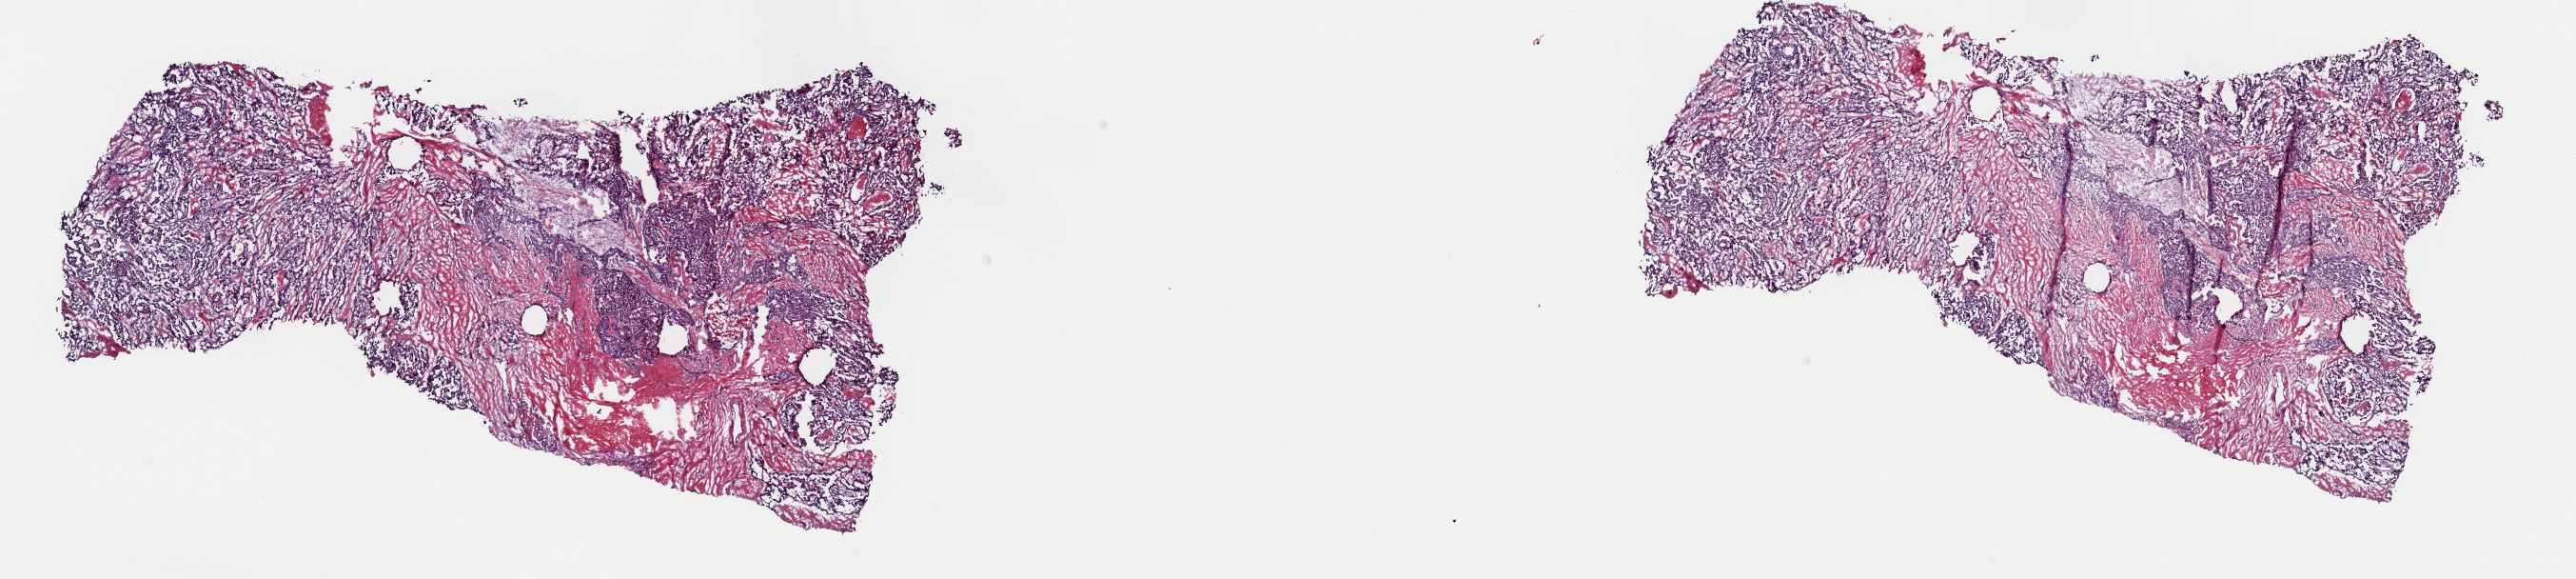
H&E-stained whole-slide image — whole scanned area (about 21.4 x 4.8 mm, slide scanned at 40x) shown as a low-resolution overview, frozen section, primary tumour sample from the thyroid. Female patient; age at initial diagnosis 64 years. Slide review estimates, as recorded: tumour cells 70%, tumour nuclei 70%, normal cells 0%, stromal cells 30%, necrosis 0%. Inflammatory infiltration, as recorded: lymphocyte infiltration 4%, monocyte infiltration 2%, neutrophil infiltration 1%.
Laterality: right. Diagnosis: Papillary adenocarcinoma, NOS (thyroid gland). TNM: T3 N1a MX. AJCC pathologic stage: III (7th edition).